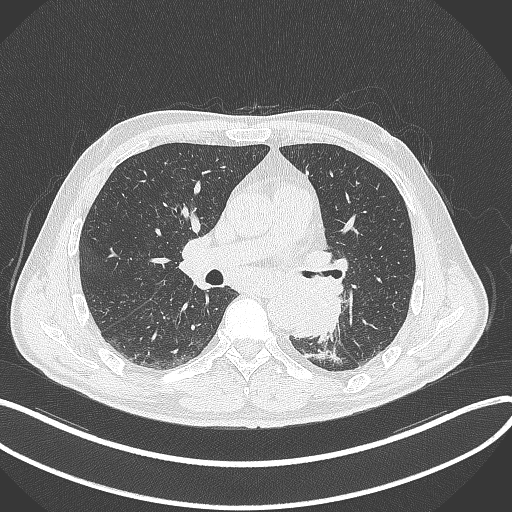
Chest CT, one axial slice. Slice 184 of 329 in the series (ordered by position). Reconstruction kernel B70f. 120 kVp. Lung window (W 1500 / L -600 HU). 1 mm slice thickness. 512 × 512 image matrix, field of view 400 × 400 mm. Patient: male, 59 years. Case-level facts recorded for this patient, not image findings: clinical TNM (as recorded): T2a N2 M0.
Structures marked on this image (bounding box drawn by a radiologist):
- lung tumour (recorded histology: squamous cell carcinoma): bounding box <289,274,345,342> (left, top, right, bottom; pixels)